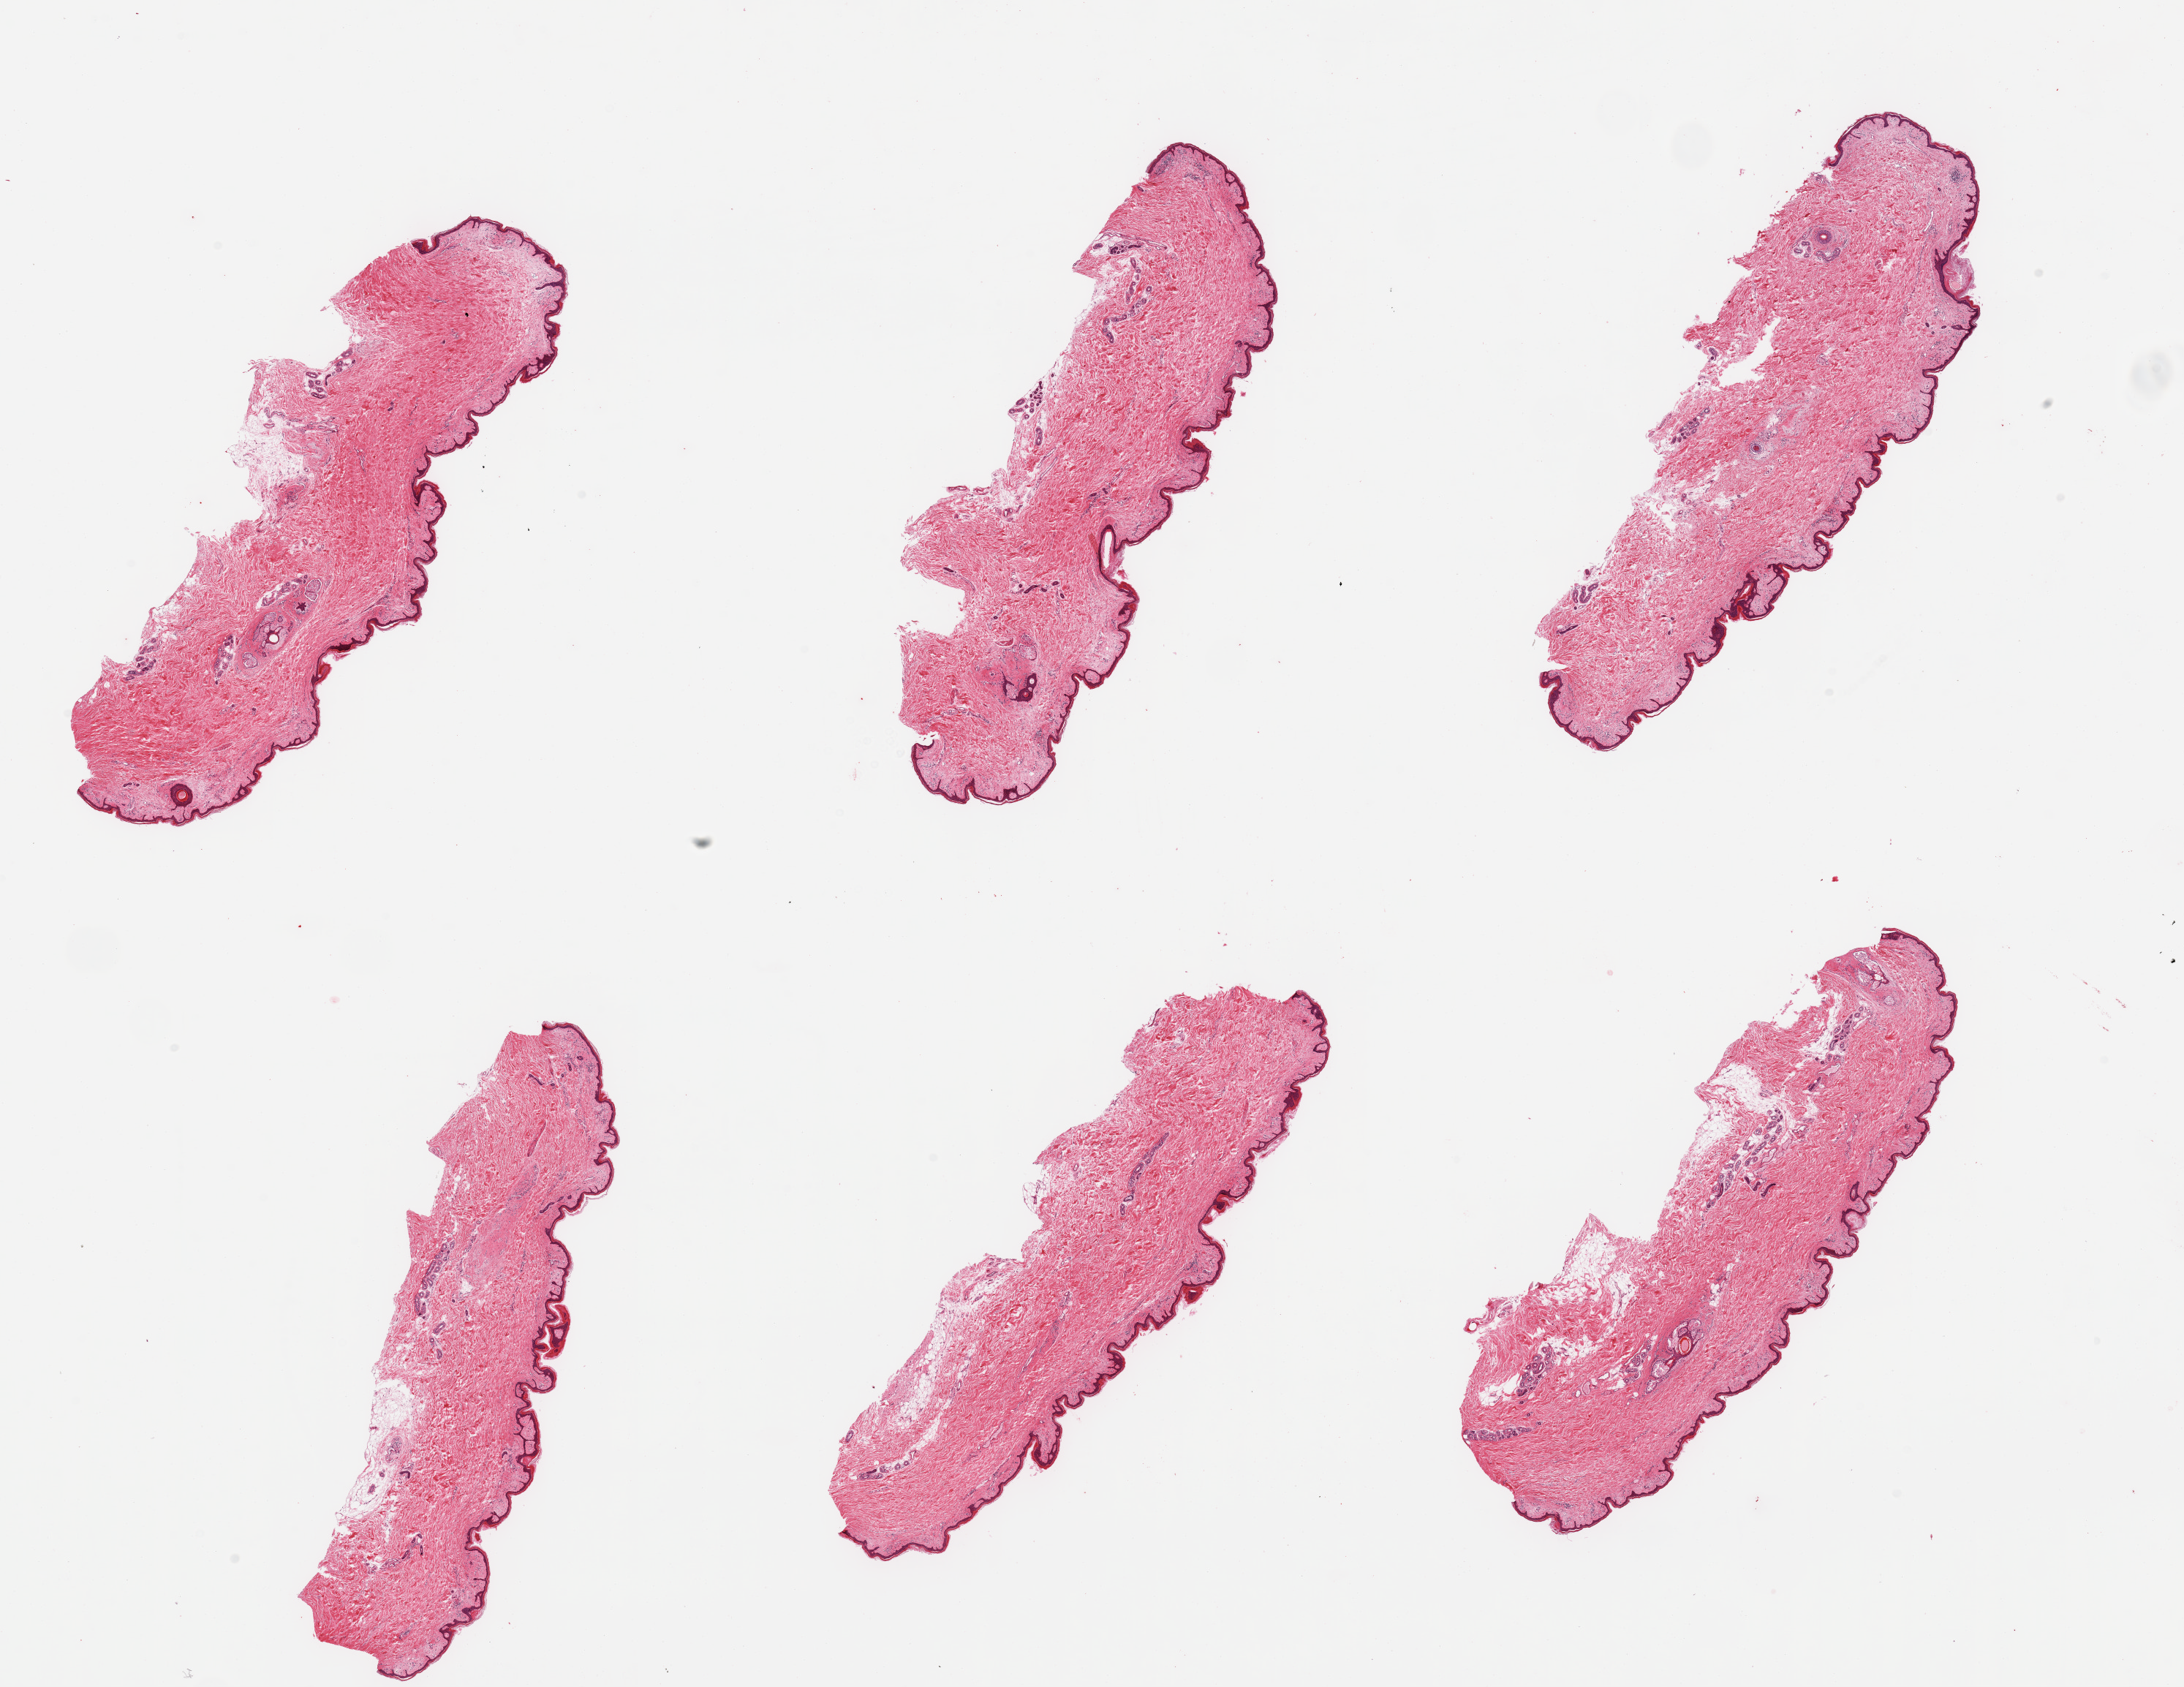
Digitized H&E-stained section, brightfield, shown as a low-resolution overview of the whole scanned area (about 23.6 x 18.2 mm), PAXgene-fixed paraffin-embedded (PFPE) section, sampled site (target tissue): skin of suprapubic region, tissue donor sample. Male donor.
* reviewer comment on this tissue sample: 6 pieces; well trimmed; 5% dermal fat